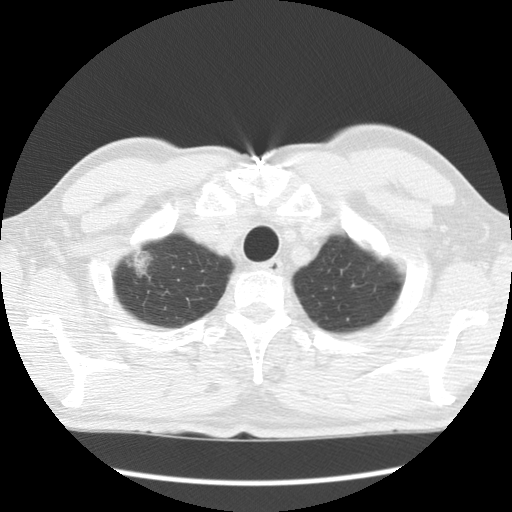
Low-dose screening chest CT, axial slice, first (baseline) screen, lung window (W 1500 / L -600 HU), standard (soft-tissue) reconstruction kernel (STANDARD), slice 12 of 132 in the series, 512 × 512 image matrix. Male, age 64 years at enrolment. Former smoker at enrolment.
- Expert-annotated lung lesion, bounding box <110,223,168,284> (left, top, right, bottom; pixels).
- The screening reader recorded 2 non-calcified nodules or masses ≥4 mm on this exam (right upper lobe, left upper lobe); which of them this box marks is not recorded.
- Official screen result: positive, change unspecified: nodule(s) >= 4 mm or enlarging nodule(s), mass(es), or other non-specific abnormalities suspicious for lung cancer.
- Lung cancer was diagnosed 750 days after this screen: adenocarcinoma, NOS, right upper lobe, well differentiated (G1), stage IB (AJCC 6th edition), 45 mm at pathology.